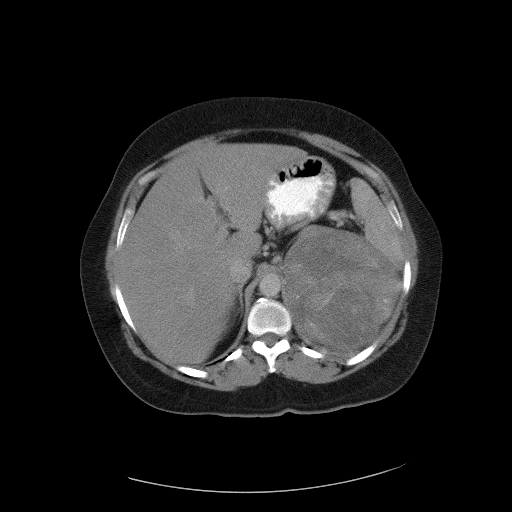
Contrast-enhanced abdominal CT, one axial slice. Slice 73 of 90 in the series (ordered by position). Reconstruction kernel FC01. Intravenous contrast given. Soft-tissue window (W 400 / L 40 HU). 5 mm slice thickness. 512 × 512 image matrix. Female patient, age 55 years. Case-level facts recorded for this patient, not image findings: diagnosis: adrenocortical carcinoma; tumour side: left adrenal; tumour size at pathology: 22 cm; Ki-67 index: 10 %; stage (as recorded): 3.
Outlined on this slice (semi-automatically segmented with operator editing):
- mass: bounding box (x1, y1, x2, y2) in pixels: (285, 227, 395, 350)